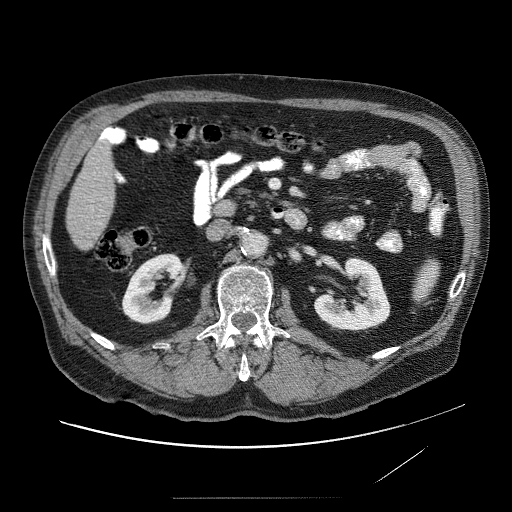
Contrast-enhanced abdominal CT (liver protocol), one axial slice. 120 kVp. Soft-tissue window (W 400 / L 40 HU). 2.5 mm slice thickness. 512 × 512 image matrix, field of view 420 × 420 mm. From the clinical record (not read from this slice): diagnosis: hepatocellular carcinoma (patient treated with transarterial chemoembolisation; whether this scan precedes or follows treatment is not stated here); TNM stage (as recorded): Stage-IVA; Child-Pugh class: A.
Structures marked on this image (semi-automatic segmentation, software-assisted and operator-edited):
- liver parenchyma outside the tumour (the mass and vessels are separate outlines, so this box may not span the whole liver): box from (x=64, y=128) to (x=122, y=254) px
- liver vessels: (x=85, y=170)–(x=109, y=216)